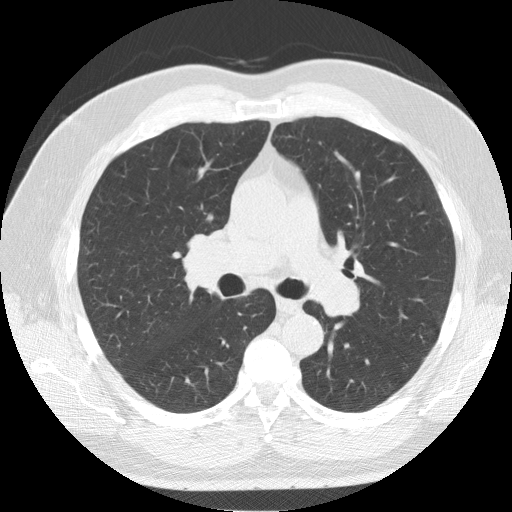
Axial slice from a low-dose chest CT screening exam, second annual screen, lung window (W 1500 / L -600 HU), 2.5 mm slice thickness, slice 53 of 139 in the series, 512 × 512 image matrix, field of view 376 × 376 mm. Male participant, aged 64 years at enrolment. Former smoker at enrolment.
Lesion marked by an expert reader, bounding box (x1, y1, x2, y2) in pixels: (165, 220, 260, 303). Screening reader's record for this exam (one nodule recorded; not confirmed to be the boxed lesion): non-calcified nodule or mass ≥4 mm, right lower lobe, 7 × 5 mm, smooth margins, soft tissue attenuation, pre-existing on the prior screen: yes; interval growth: no. Official screen result: positive, other. Participant outcome: lung cancer diagnosed 63 days after this screen — adenocarcinoma, NOS, right upper lobe, poorly differentiated (G3), stage IB (AJCC 6th edition), 37 mm at pathology.